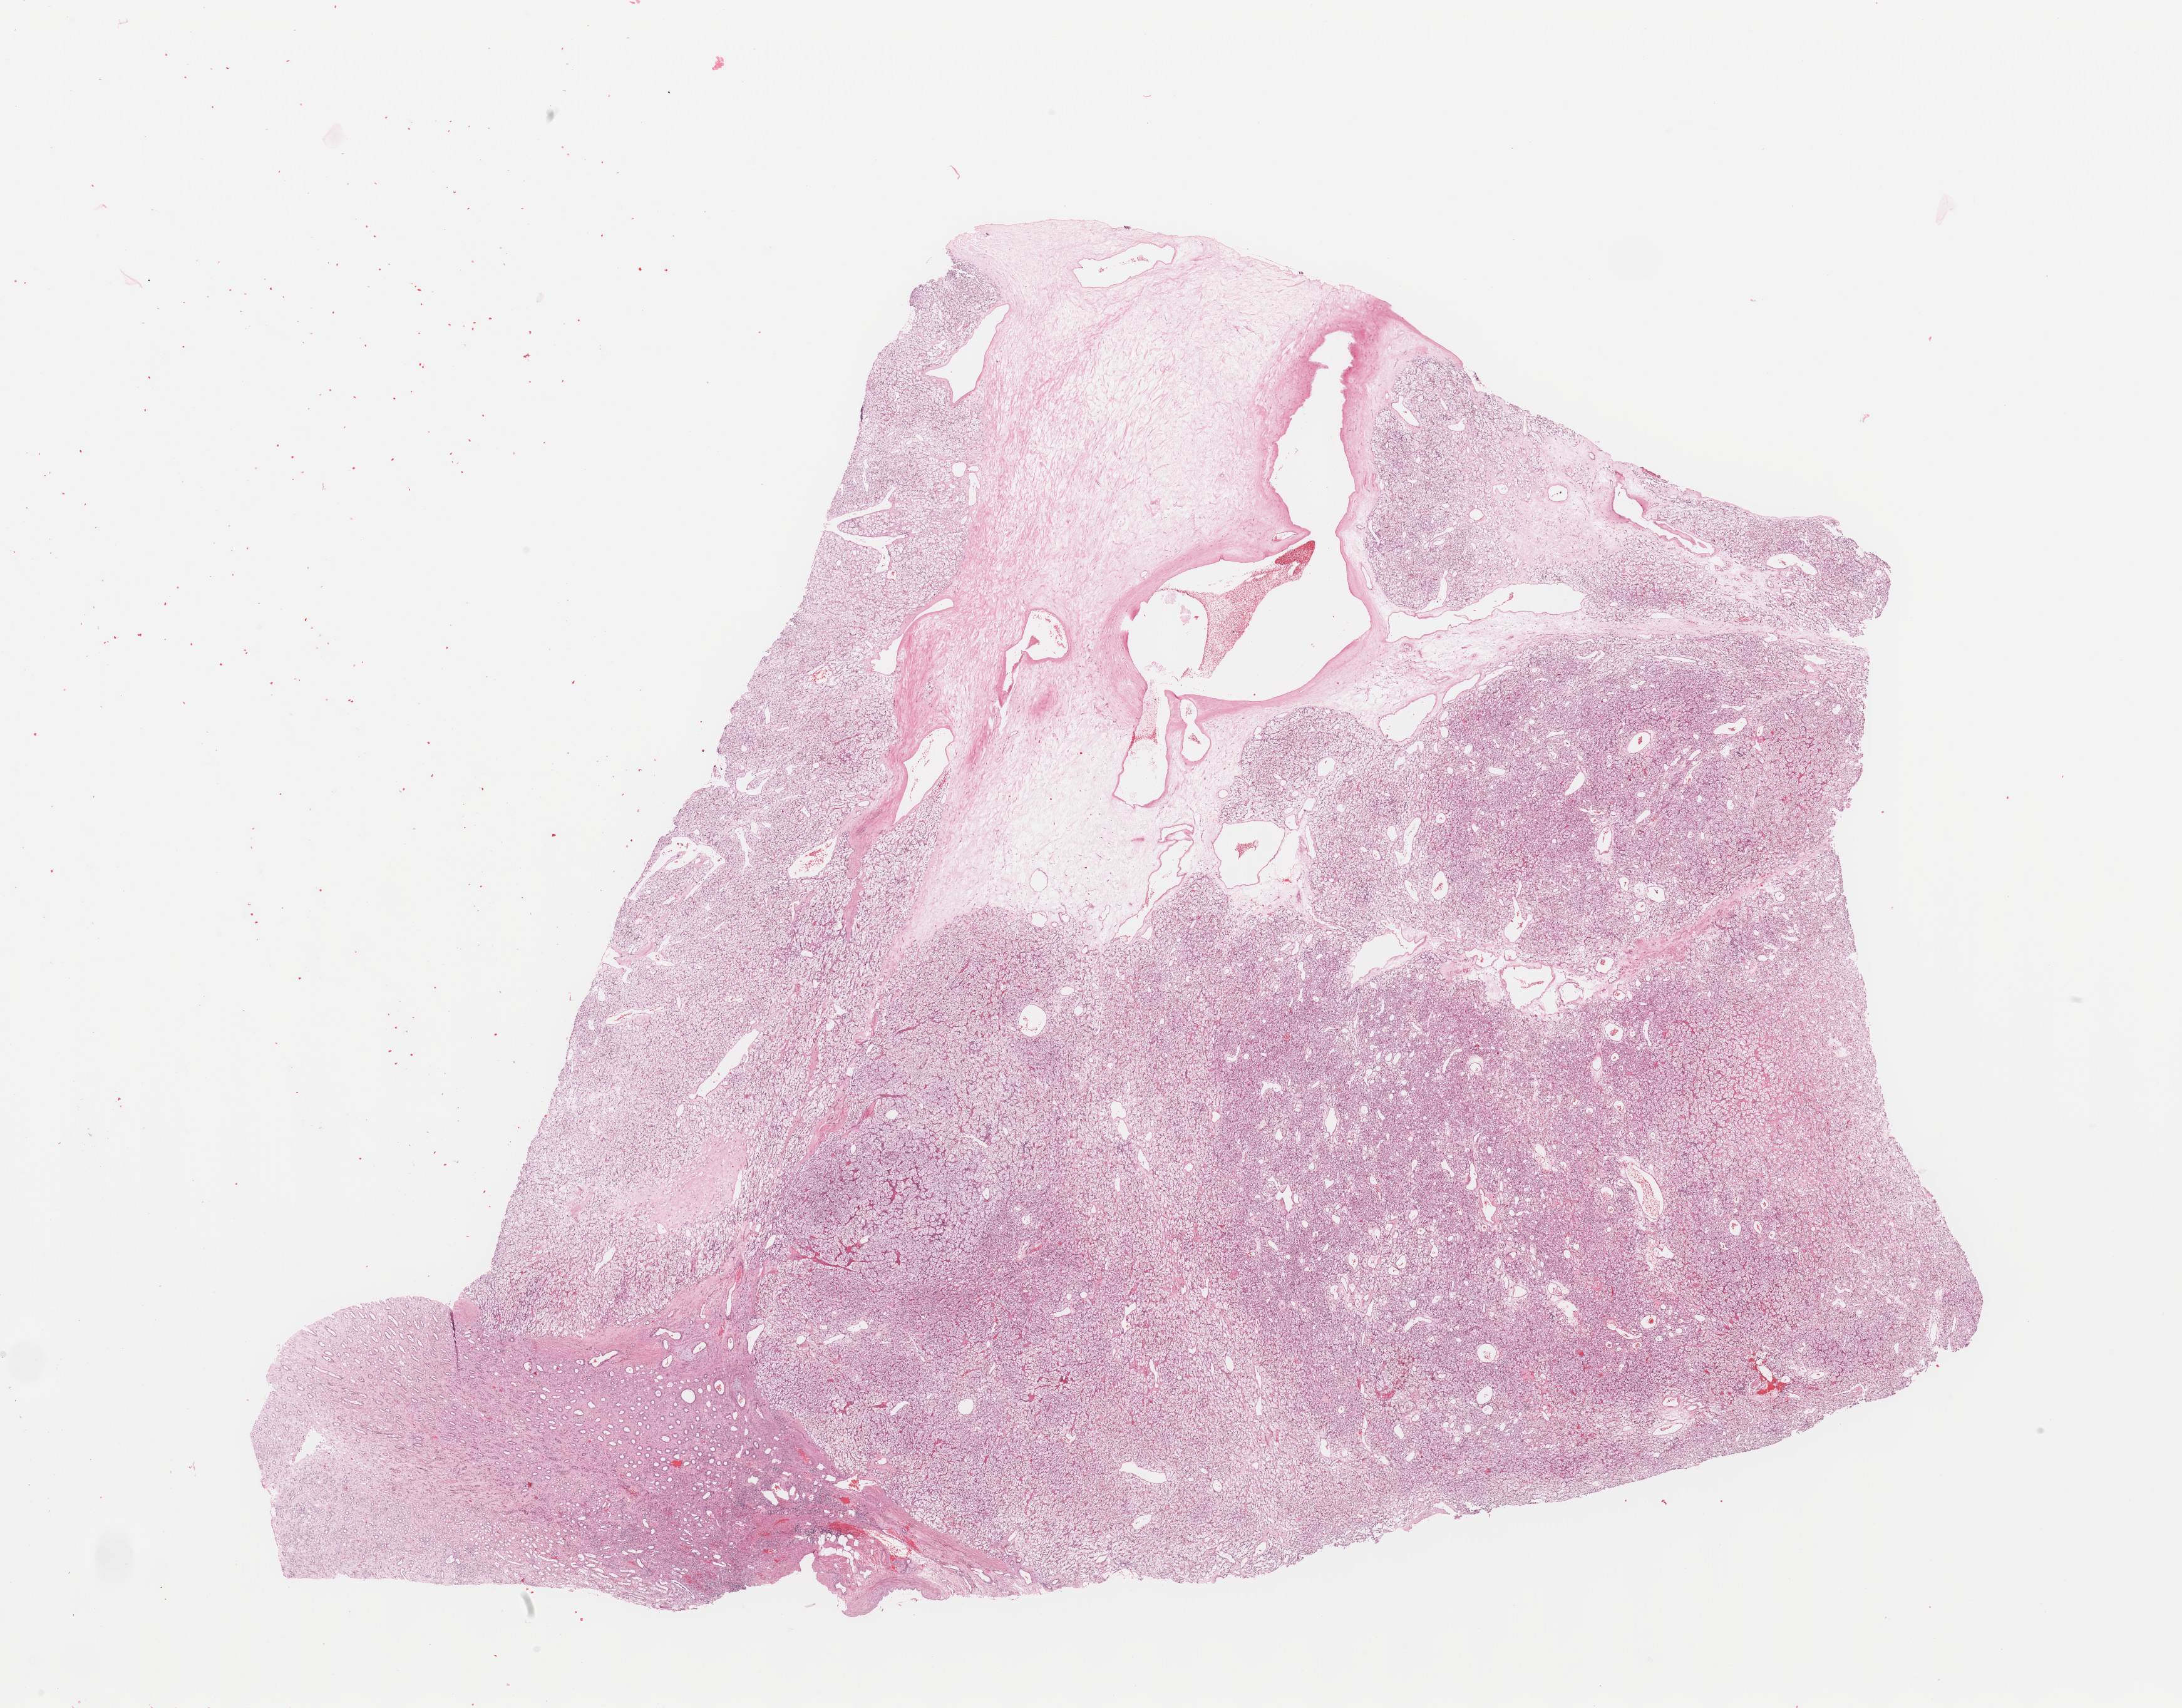
H&E-stained whole-slide image — whole scanned area (about 27.6 x 21.6 mm, from a 20x scan) shown as a low-resolution overview, kidney, tumour tissue. 69-year-old female patient. Histologic grade: G2 (moderately differentiated).
Histologic diagnosis: Renal cell carcinoma, NOS.